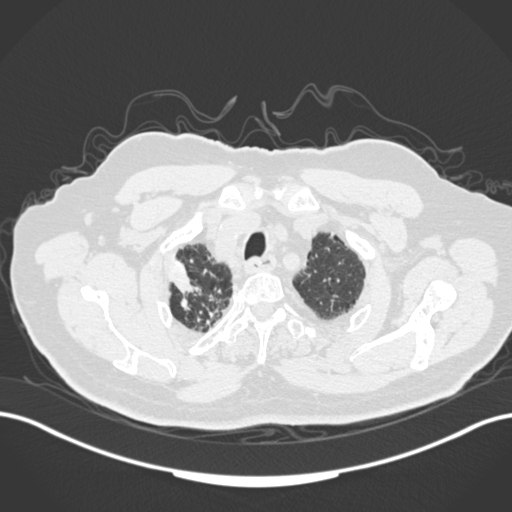
Chest CT, one axial slice; position 151 of 205 along the scan axis; reconstruction kernel B30f; 120 kVp; lung window (W 1500 / L -600 HU); 1 mm slice thickness; 512 × 512 image matrix. Male patient, age 72 years. From the clinical record (not read from this slice): clinical TNM (as recorded): T1a N0 M0.
Outlined on this slice (bounding box drawn by a radiologist):
- lung tumour (recorded histology: squamous cell carcinoma): bounding box <168,253,205,313> (left, top, right, bottom; pixels)